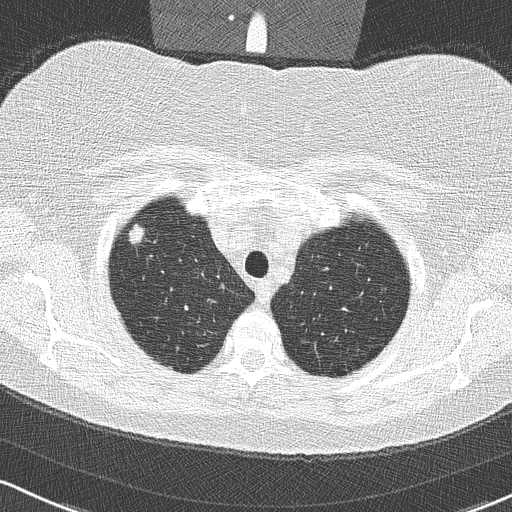
Axial slice from a low-dose chest CT screening exam. Third annual screen. Lung window (W 1500 / L -600 HU). 2 mm slice thickness. Slice 45 of 315 in the series. Female participant, aged 58 years at enrolment. Former smoker at enrolment.
Lesion marked by an expert reader, bounding box [x1, y1, x2, y2] px = [119, 219, 159, 258]. The screening reader recorded 2 non-calcified nodules or masses ≥4 mm on this exam (right upper lobe, right lower lobe); which of them this box marks is not recorded. Official screen result: positive, other. Later outcome: lung cancer diagnosed 48 days after this screen — bronchiolo-alveolar adenocarcinoma, NOS, right upper lobe, well differentiated (G1), stage IA (AJCC 6th edition), 9 mm at pathology.